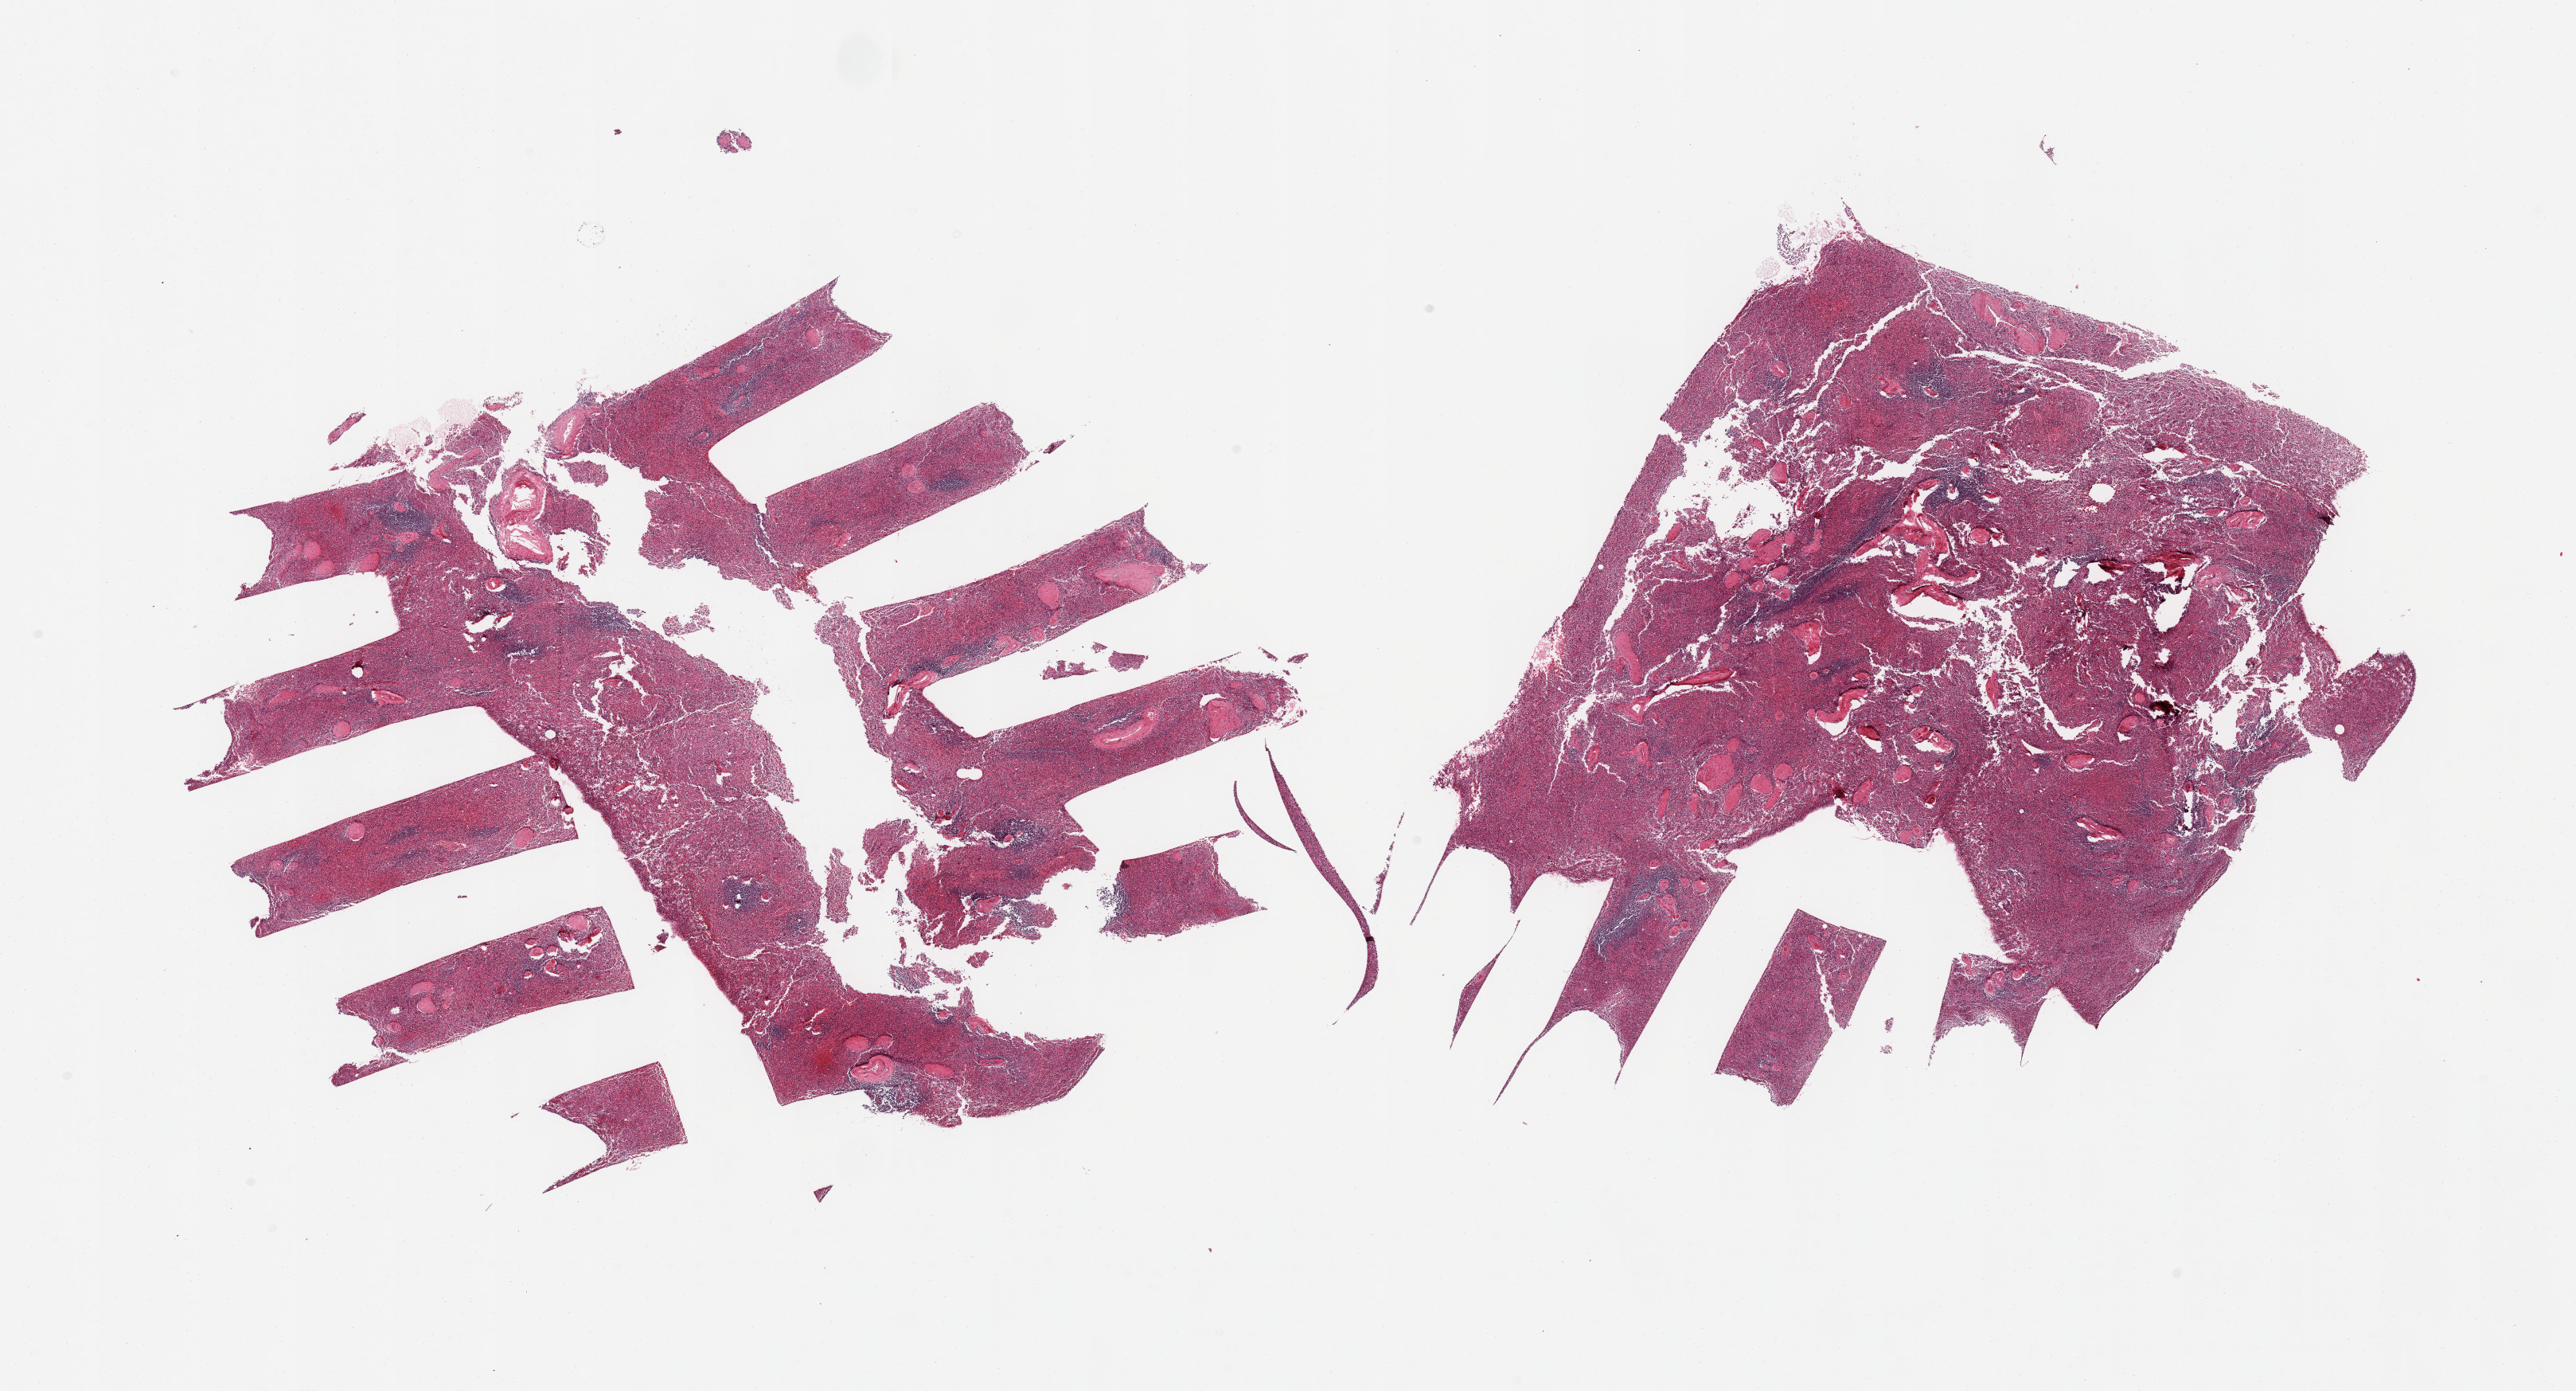
Digitized haematoxylin and eosin-stained section, low-resolution overview of the scanned area, about 25.6 x 13.8 mm (acquisition: 20x scan). PAXgene-fixed, paraffin-embedded tissue. Section of spleen (target tissue). Donor tissue sample. Female donor.
Reviewer comment on this tissue sample: 2 pieces, moderate congestion.